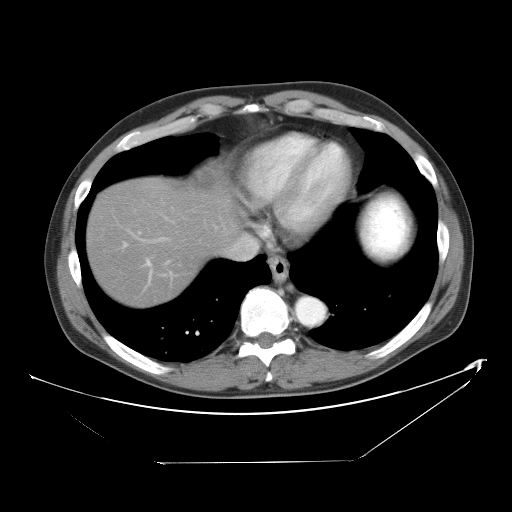
Contrast-enhanced abdominal CT, one axial slice. Slice 47 of 53 in the series (ordered by position). 120 kVp. Intravenous contrast given. Soft-tissue window (W 400 / L 40 HU). 512 × 512 image matrix, field of view 438 × 438 mm. Male patient, age 59 years. Case-level facts recorded for this patient, not image findings: diagnosis: colorectal cancer liver metastases, imaged before liver resection.
Outlined on this slice (expert manual segmentation):
- hepatic veins: bounding box (x1, y1, x2, y2) in pixels: (231, 236, 258, 260)
- liver: (89, 166, 237, 305)
- planned liver remnant (the part of the liver to remain after resection): (90, 183, 216, 305)
- portal vein (with intrahepatic branches): (146, 260, 152, 281)
- liver metastasis: (180, 169, 227, 194)